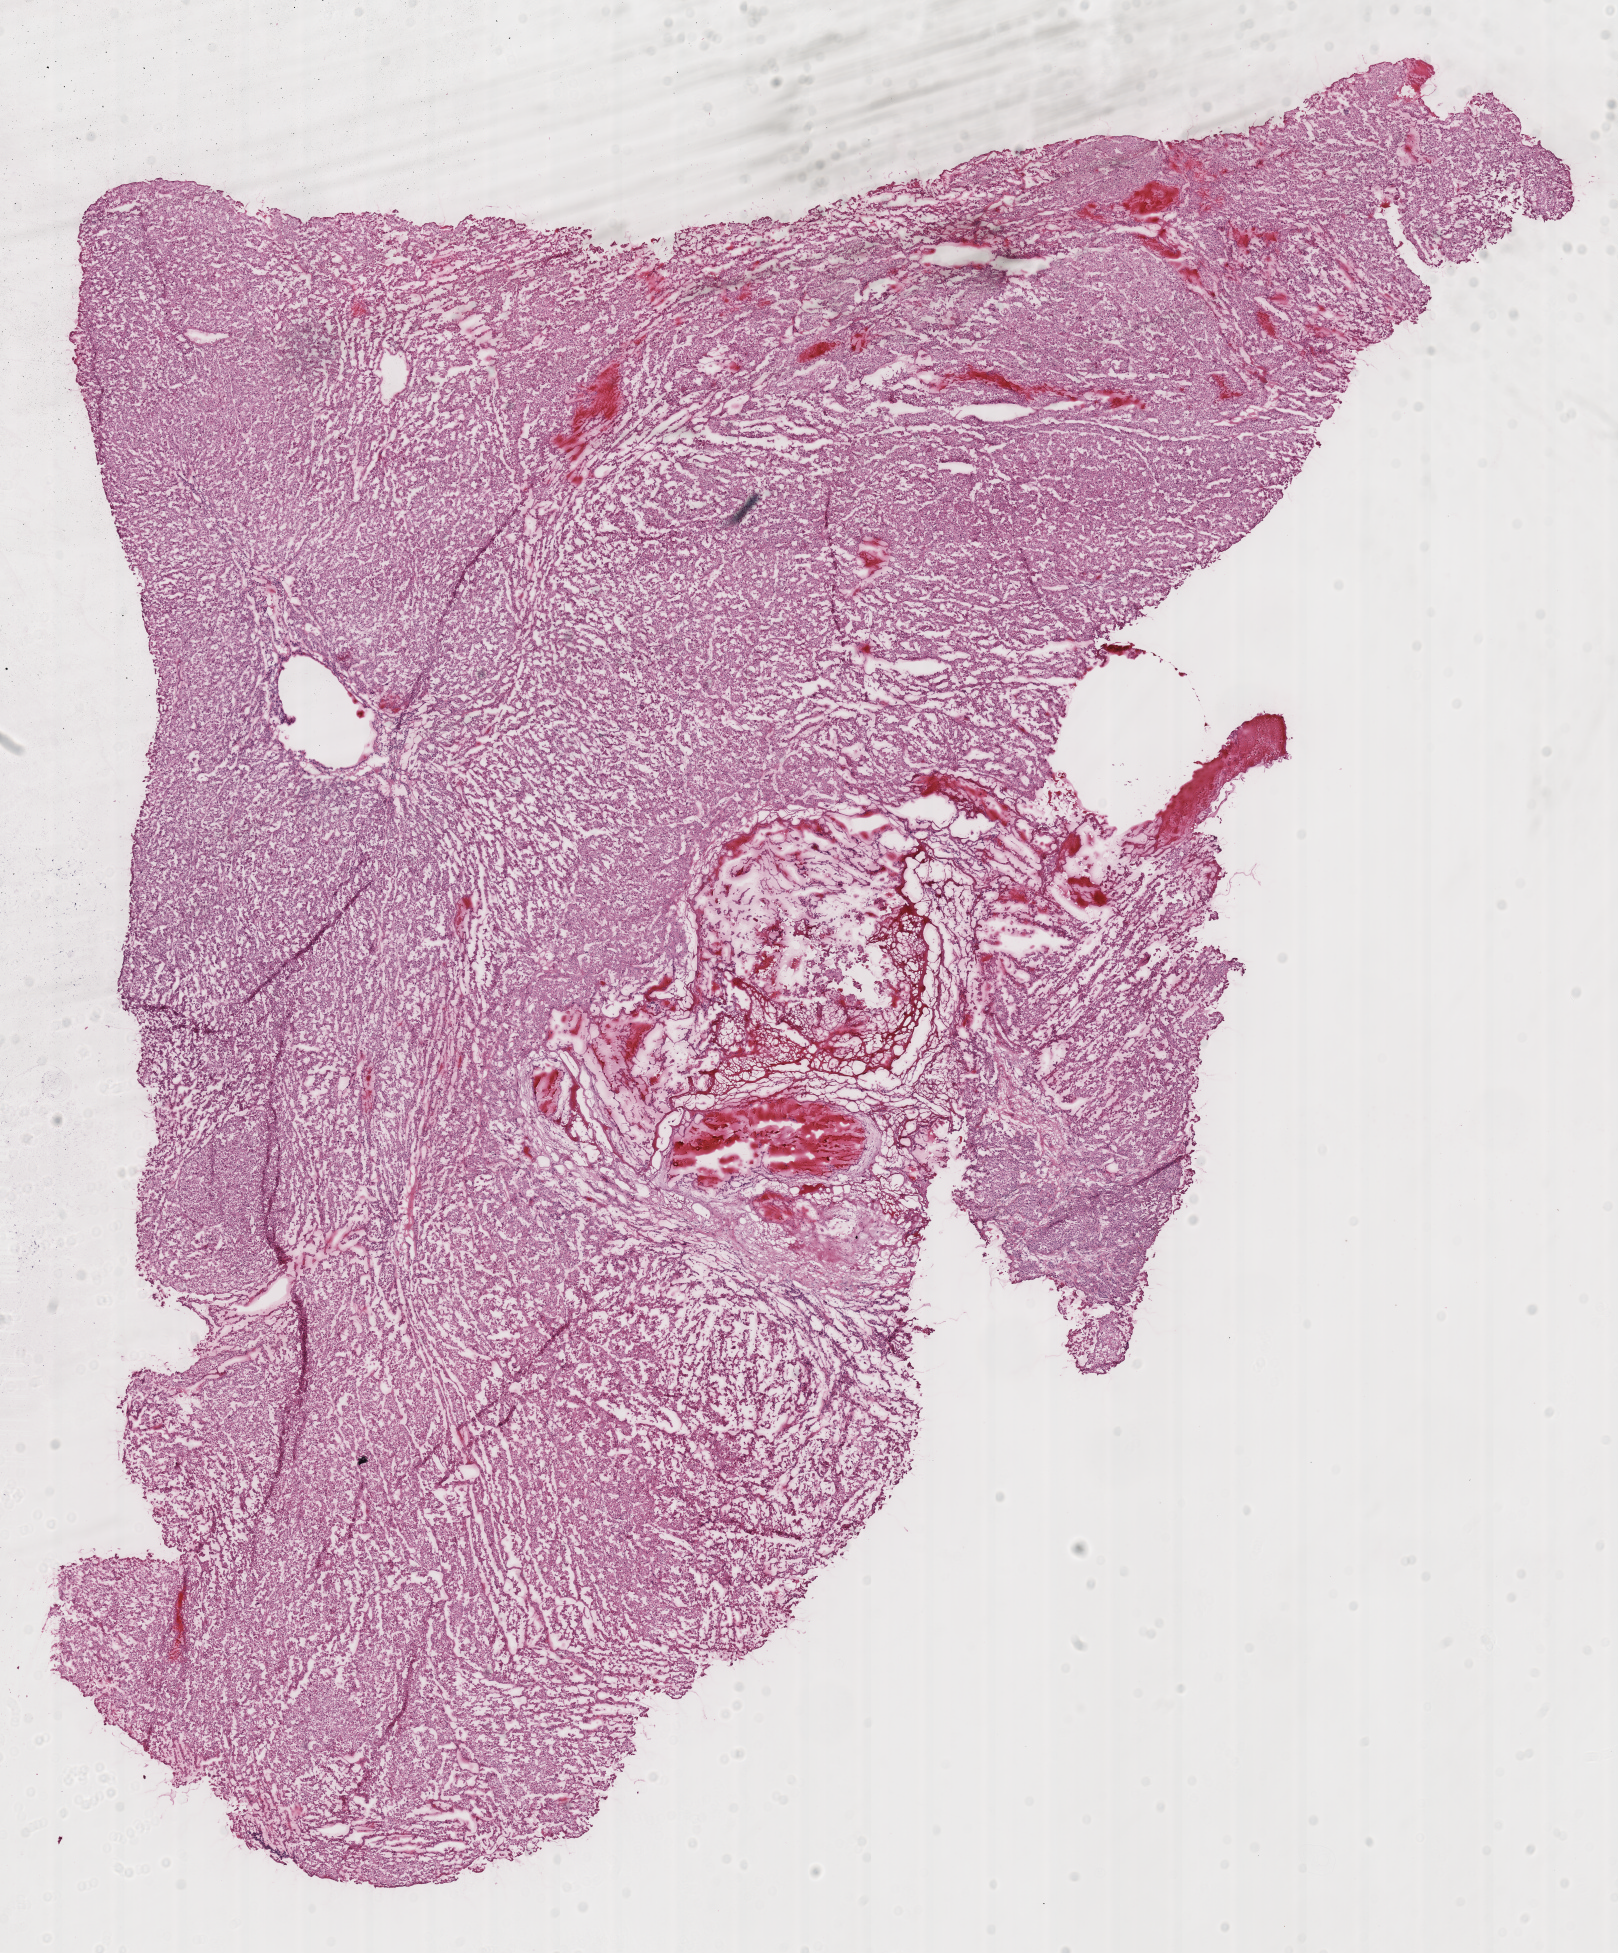
Hematoxylin and eosin (H&E) stained whole-slide image — a low-resolution overview of the entire scanned area, about 12.7 x 15.4 mm (slide scanned at 40x). Frozen section from the top of the tissue portion. Primary tumour sample from the kidney. Patient: male, age at initial diagnosis 75 years. Pathologist review of this section (percent, as recorded): tumour cells 100%, tumour nuclei 95%, normal cells 0%, stromal cells 0%, necrosis 0%. Inflammatory infiltration, as recorded: lymphocyte infiltration 0%, monocyte infiltration 0%, neutrophil infiltration 0%.
• AJCC pathologic stage: I (6th edition)
• pathologic diagnosis: Renal cell carcinoma, chromophobe type